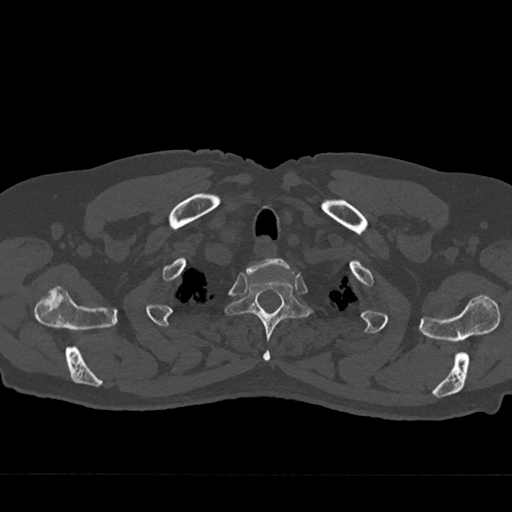
CT including the spine, one axial slice; slice 621 of 797 in the series (ordered by position); reconstruction kernel Br40s/3; bone window (W 1800 / L 400 HU); 0.5 mm slice thickness; 512 × 512 image matrix. Patient: male, 75 years. From the clinical record (not read from this slice): primary cancer: renal.
Outlined on this slice (semi-automatic segmentation, software-assisted and operator-edited):
- T1 vertebra: bounding box <246,258,294,277> (left, top, right, bottom; pixels)
- T2 vertebra: <224,278,312,361>